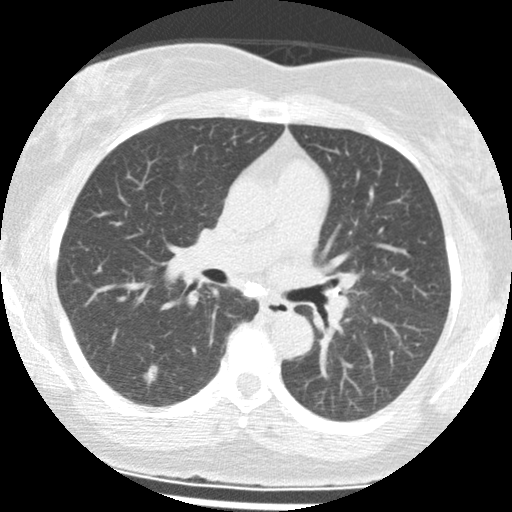
Chest CT (low-dose screening protocol), one axial image; baseline screening round; lung window (W 1500 / L -600 HU); 2.5 mm slice thickness; standard (soft-tissue) reconstruction kernel (STANDARD); slice 51 of 124 in the series. Female, age 65 years at enrolment. Current smoker at enrolment.
Lesion marked by an expert reader, bounding box <131,356,168,391> (left, top, right, bottom; pixels). Screening reader's record for this exam (one nodule recorded; not confirmed to be the boxed lesion): non-calcified nodule or mass ≥4 mm, right lower lobe, 8 × 6 mm, poorly defined margins, mixed attenuation. Official screen result: positive, change unspecified: nodule(s) >= 4 mm or enlarging nodule(s), mass(es), or other non-specific abnormalities suspicious for lung cancer.